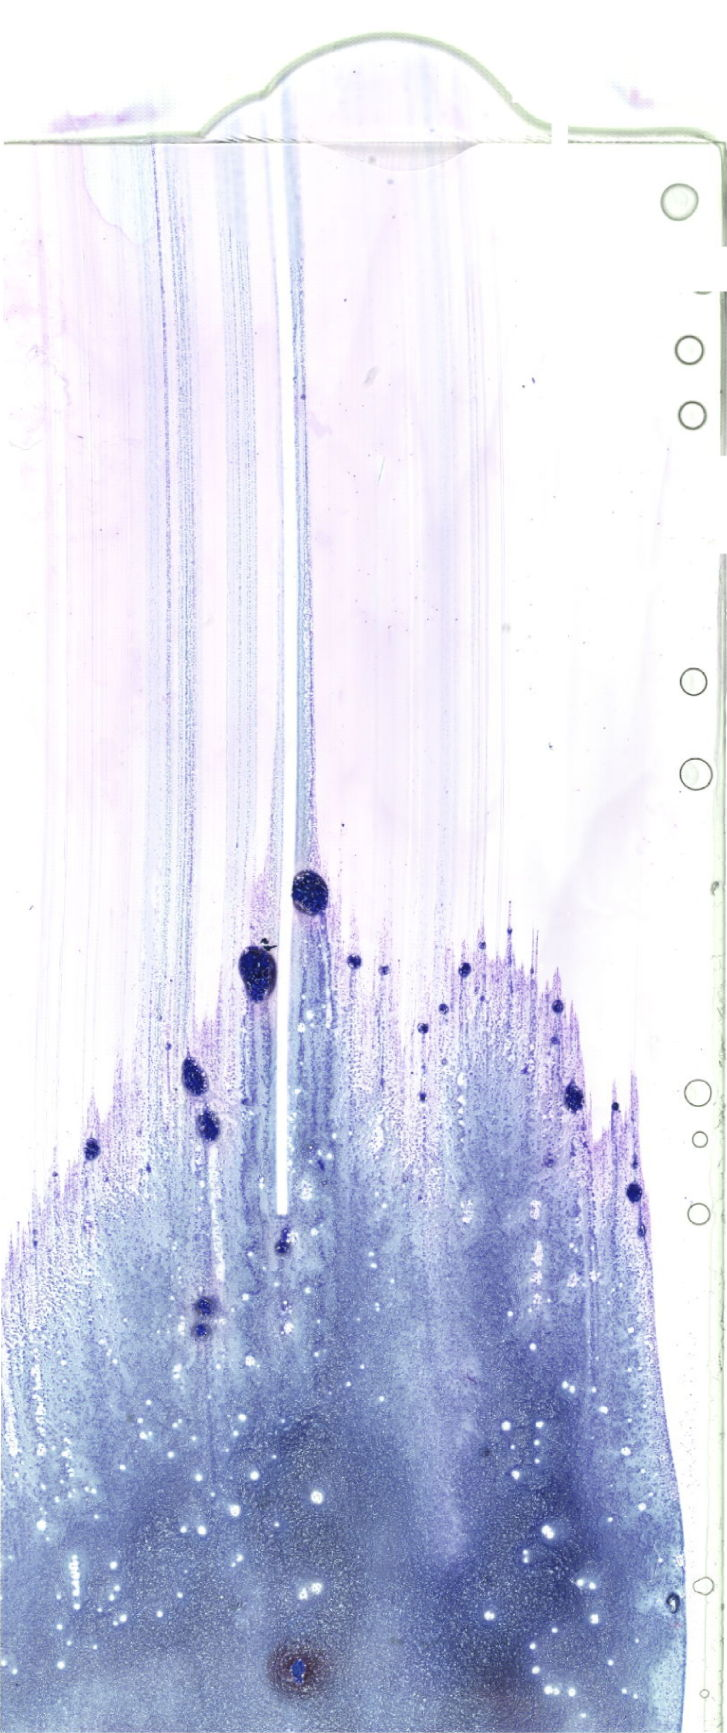
Bone marrow aspirate smear, May-Grünwald–Giemsa stain, whole-slide image — shown as a low-resolution overview of the whole scanned area (about 20.6 x 49.1 mm). Male patient.
Diagnosis: Acute Myeloid Leukemia with Minimal Differentiation.